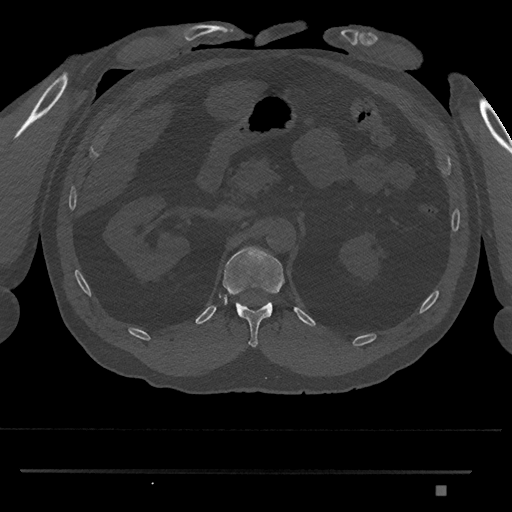
CT including the spine, one axial slice. Position 875 of 1134 along the scan axis. 120 kVp. Bone window (W 1800 / L 400 HU). 0.5 mm slice thickness. 512 × 512 image matrix, field of view 429 × 429 mm. Patient: male, 65 years. From the clinical record (not read from this slice): primary cancer: prostate.
Structures marked on this image (semi-automatically segmented with operator editing):
- T12 vertebra: bounding box <222,247,285,347> (left, top, right, bottom; pixels)